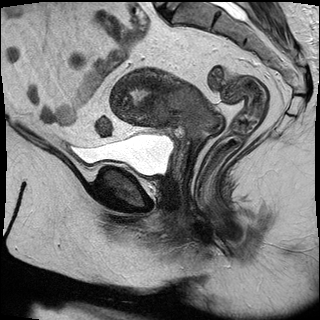
Pelvic MRI for cervical cancer, one sagittal slice. Position 15 of 30 along the scan axis. T2-weighted. 1.5 T. TE 89 ms, TR 2930 ms. 320 × 320 image matrix, field of view 260 × 260 mm. Female patient, age 53 years.
Structures marked on this image (expert manual segmentation):
- uterus and cervix: bounding box (x1, y1, x2, y2) in pixels: (111, 67, 222, 140)